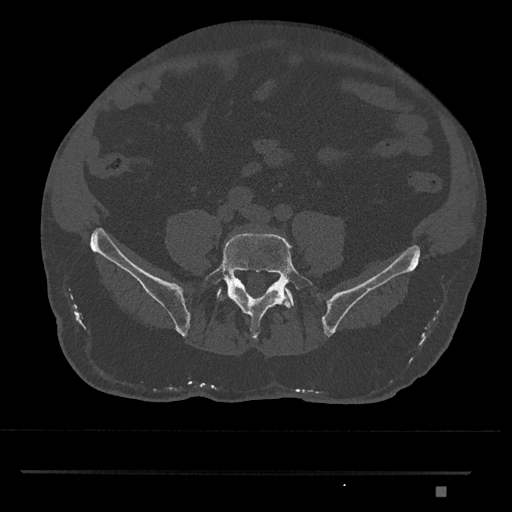
CT including the spine, one axial slice; slice 556 of 1134 in the series (ordered by position); reconstruction kernel Br40s/3; bone window (W 1800 / L 400 HU); 0.5 mm slice thickness; 512 × 512 image matrix, field of view 429 × 429 mm. Patient: male, 65 years. Case-level facts recorded for this patient, not image findings: primary cancer: prostate.
Annotated regions visible in this slice (semi-automatic segmentation, software-assisted and operator-edited):
- L5 vertebra: bounding box (x1, y1, x2, y2) in pixels: (205, 232, 315, 340)